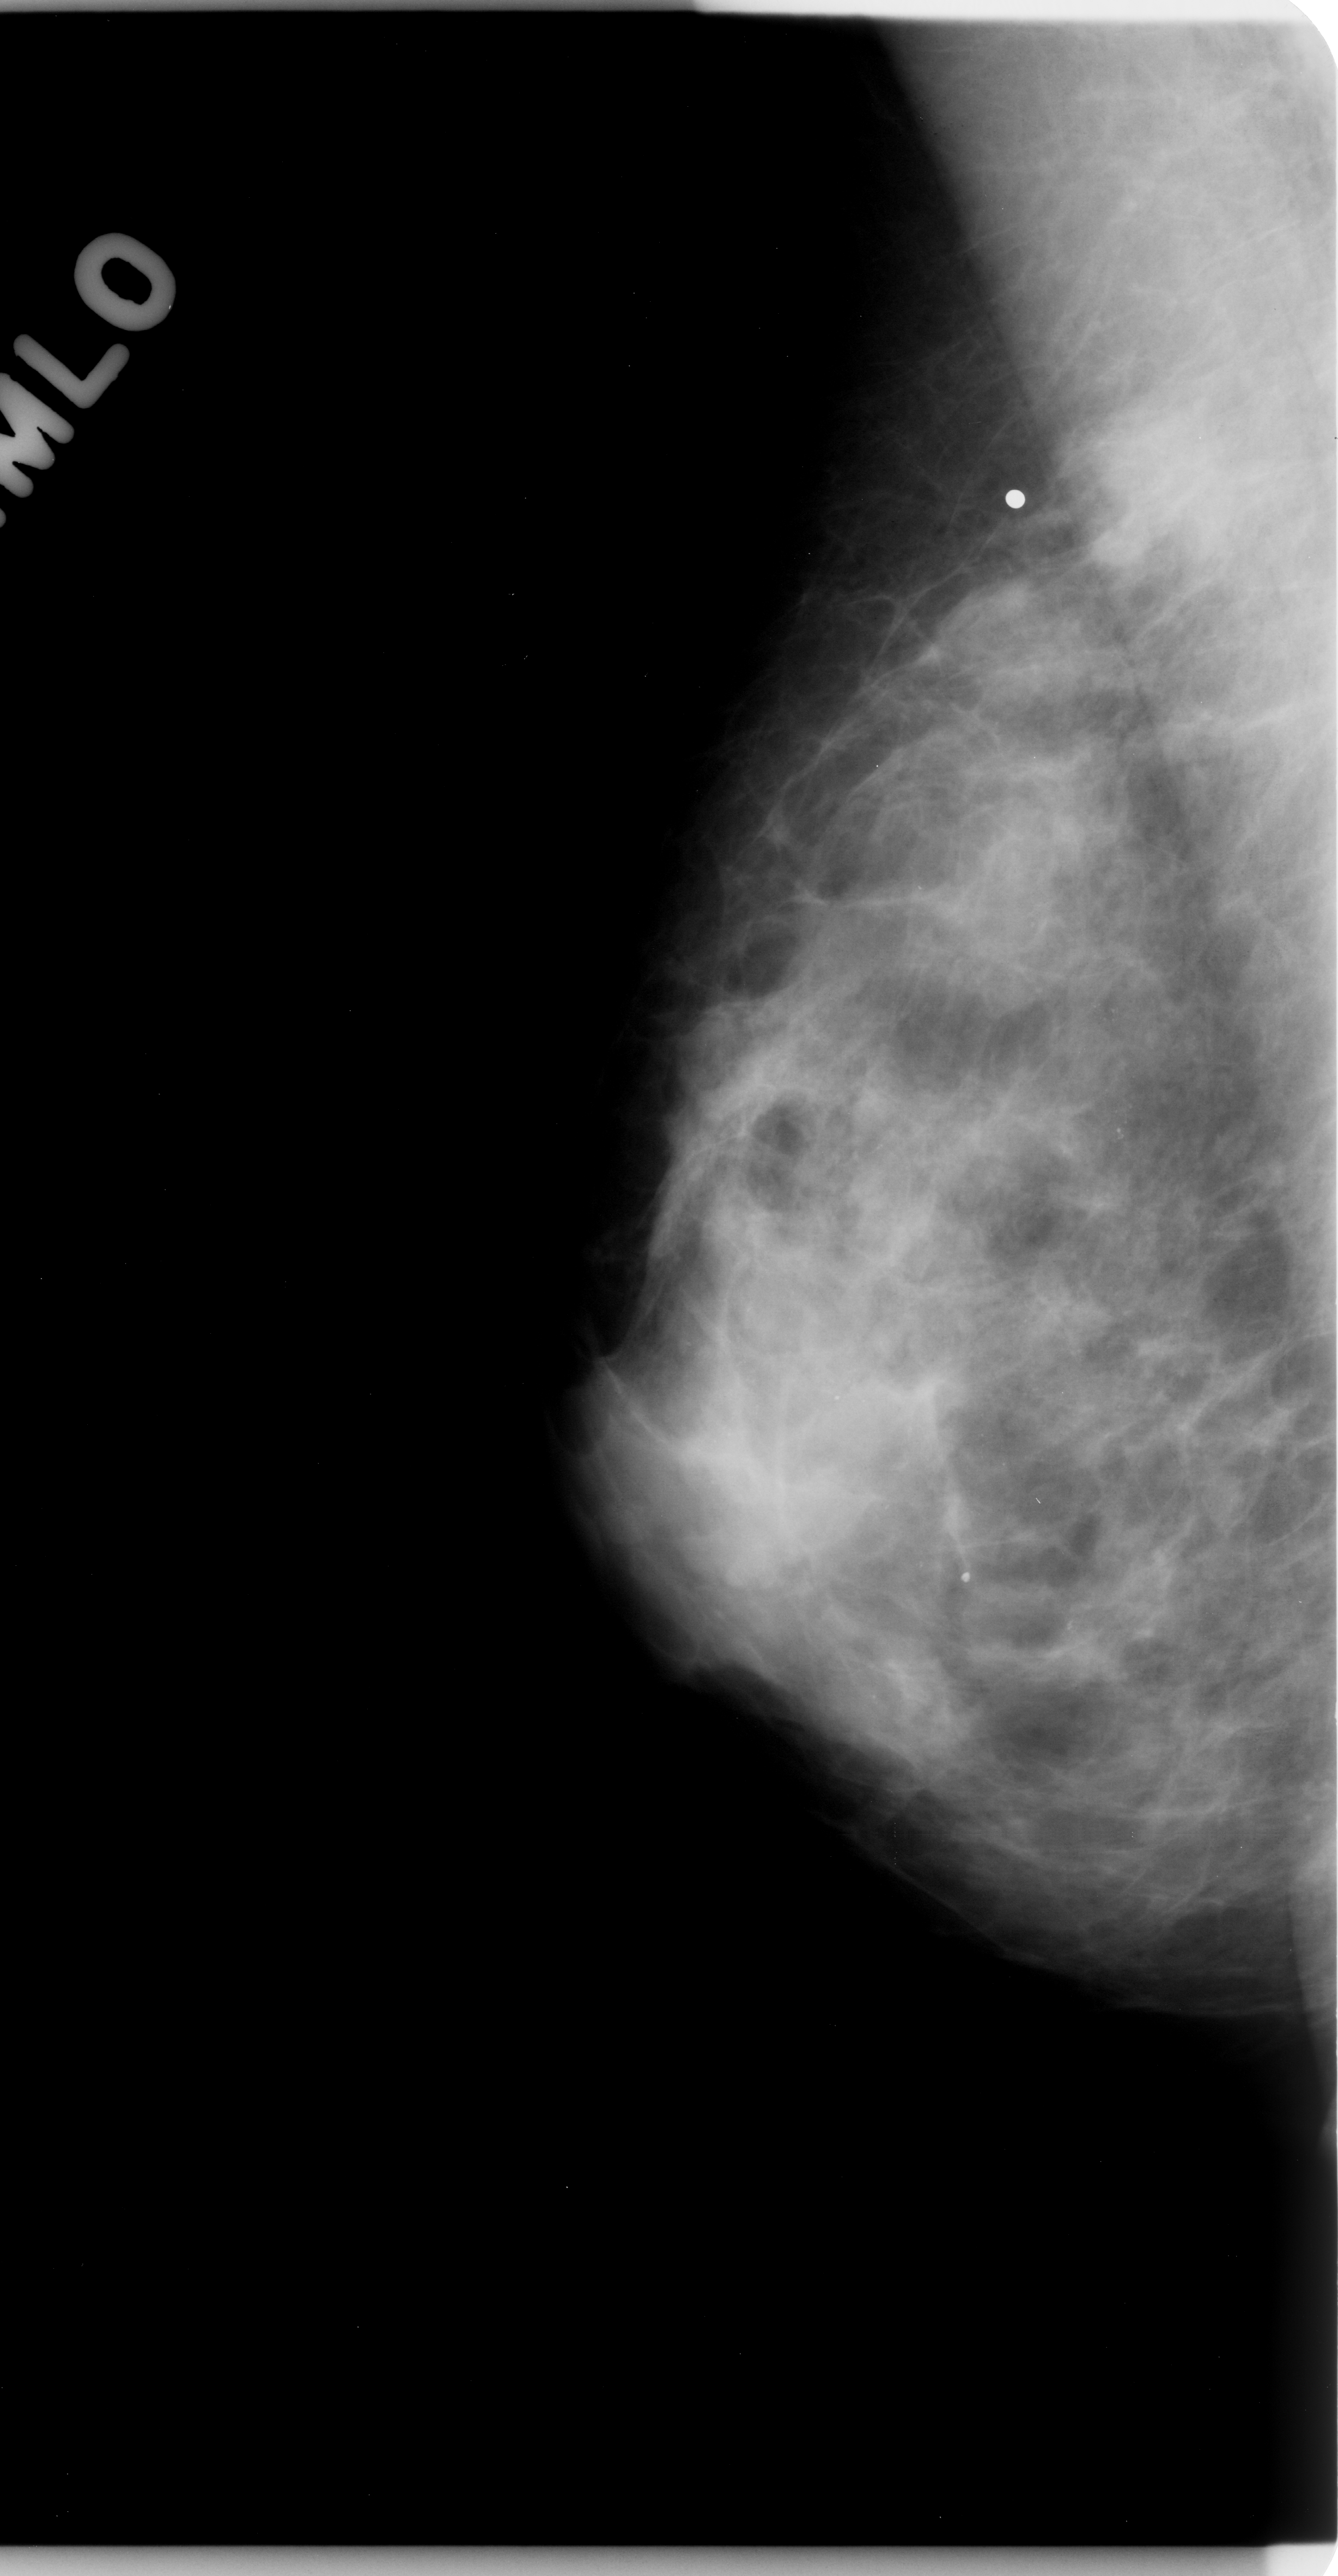
Digitized screen-film mammogram, right breast, MLO view, BI-RADS breast density category 3 (scale 1–4).
Abnormality record for this image: mass, shape irregular, margins ill defined; BI-RADS assessment category 4; pathology (as recorded): malignant.